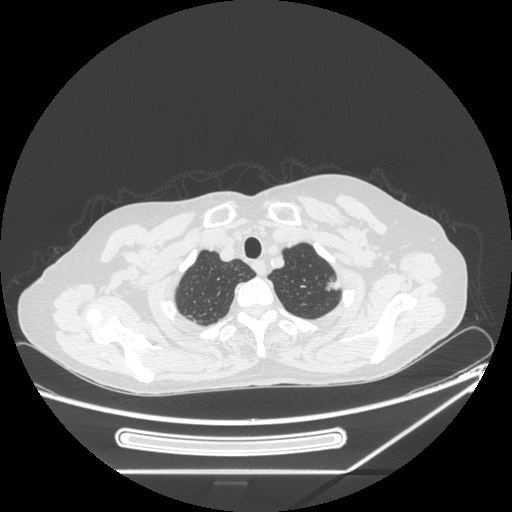
Chest CT, one axial slice. Position 215 of 250 along the scan axis. Reconstruction kernel STANDARD. 120 kVp. Lung window (W 1500 / L -600 HU). 512 × 512 image matrix, field of view 409 × 409 mm. Female patient, age 57 years. From the clinical record (not read from this slice): clinical TNM (as recorded): T1c N0 M0.
Outlined on this slice (bounding box drawn by a radiologist):
- lung tumour (recorded histology: adenocarcinoma): bounding box <322,274,344,295> (left, top, right, bottom; pixels)